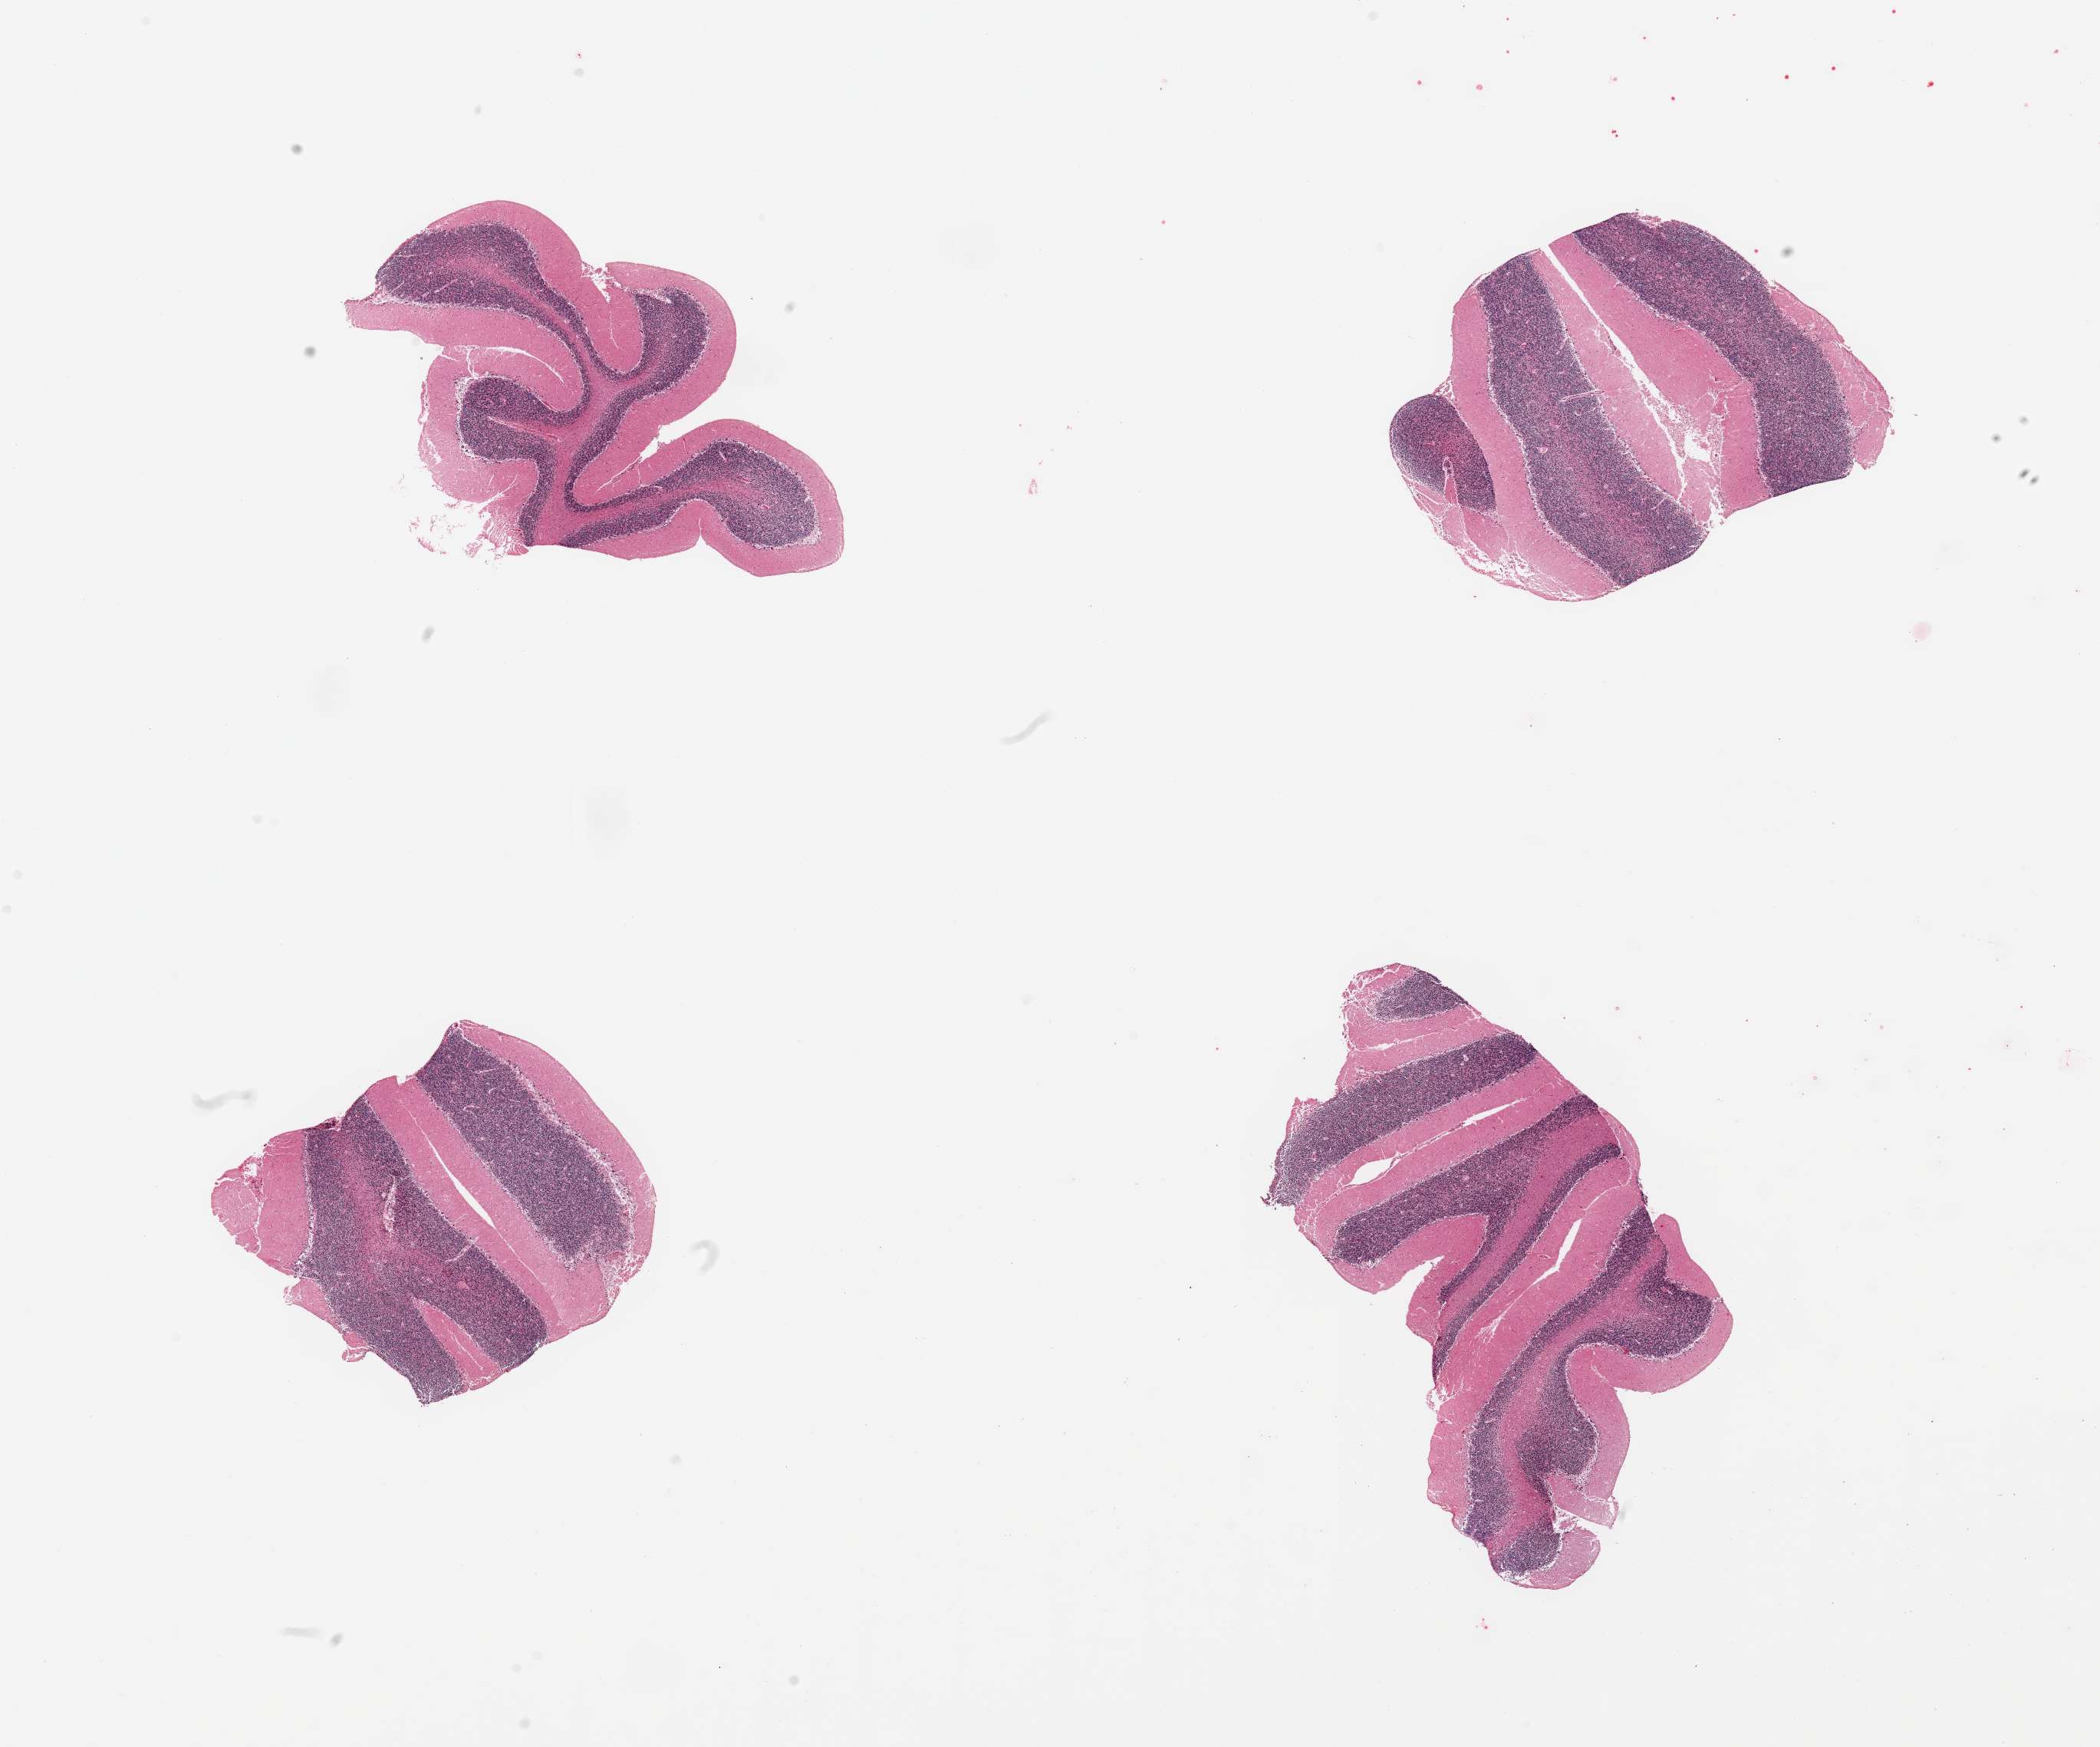
H&E whole-slide image — a low-resolution overview of the entire scanned area, about 21.7 x 18.0 mm; PAXgene-fixed paraffin-embedded (PFPE) section; sampled site (target tissue): cerebellum; donor tissue sample.
- reviewer comment on this tissue sample: 4 pieces